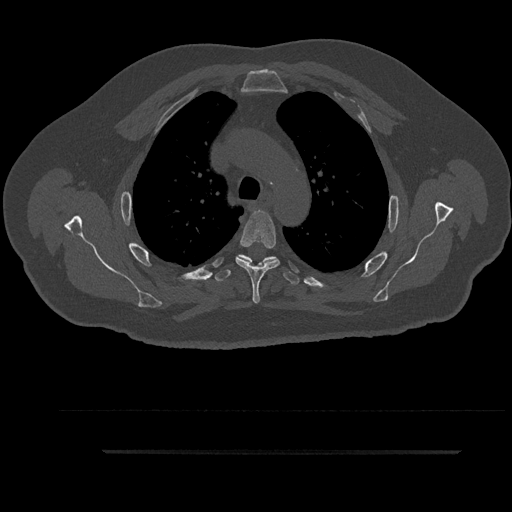
CT including the spine, one axial slice; slice 664 of 797 in the series (ordered by position); bone window (W 1800 / L 400 HU); 0.5 mm slice thickness; 512 × 512 image matrix, field of view 432 × 432 mm. Male patient, age 63 years. Case-level facts recorded for this patient, not image findings: primary cancer: renal; vertebrae with lytic lesions (as recorded): T8.
Outlined on this slice (semi-automatic segmentation, software-assisted and operator-edited):
- T4 vertebra: box from (x=235, y=210) to (x=280, y=304) px
- T5 vertebra: (x=214, y=254)–(x=299, y=285)